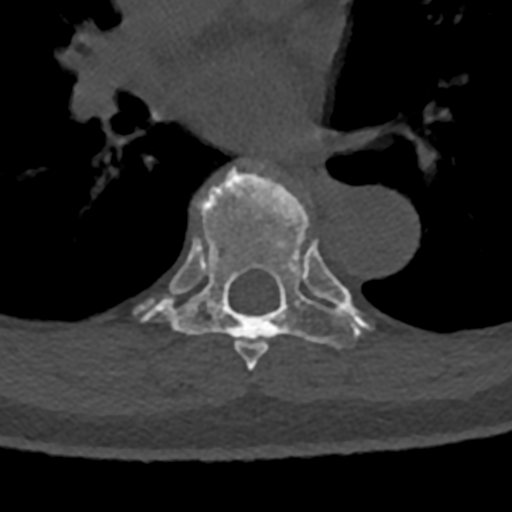
CT including the spine, one axial slice. Position 773 of 797 along the scan axis. Reconstruction kernel Br40s/3. Bone window (W 1800 / L 400 HU). 0.5 mm slice thickness. 512 × 512 image matrix, field of view 160 × 160 mm. Male patient, age 74 years. From the clinical record (not read from this slice): primary cancer: renal; vertebrae with lytic lesions (as recorded): T10, L1, L2, L3, L4, L5.
Annotated regions visible in this slice (semi-automatic segmentation, software-assisted and operator-edited):
- T6 vertebra: bounding box <235,341,268,371> (left, top, right, bottom; pixels)
- T7 vertebra: <134,163,370,357>